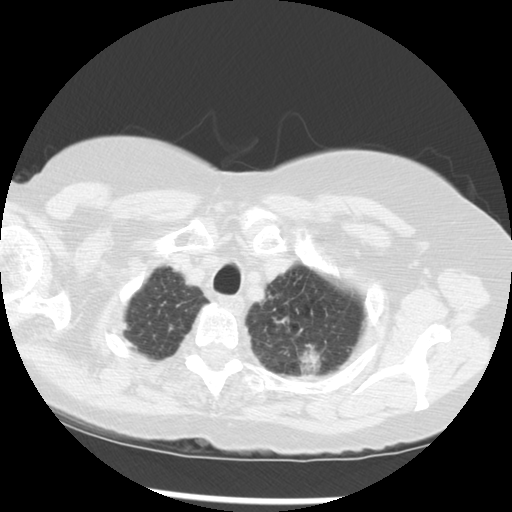
Low-dose screening chest CT, one axial slice; position 249 of 283 along the scan axis; reconstruction kernel STANDARD; 120 kVp; lung window (W 1500 / L -600 HU); 2.5 mm slice thickness; 512 × 512 image matrix.
Annotated regions visible in this slice (manually delineated by an expert):
- lesion 1 (tumor, upper lobe of left lung): box from (x=300, y=345) to (x=322, y=375) px